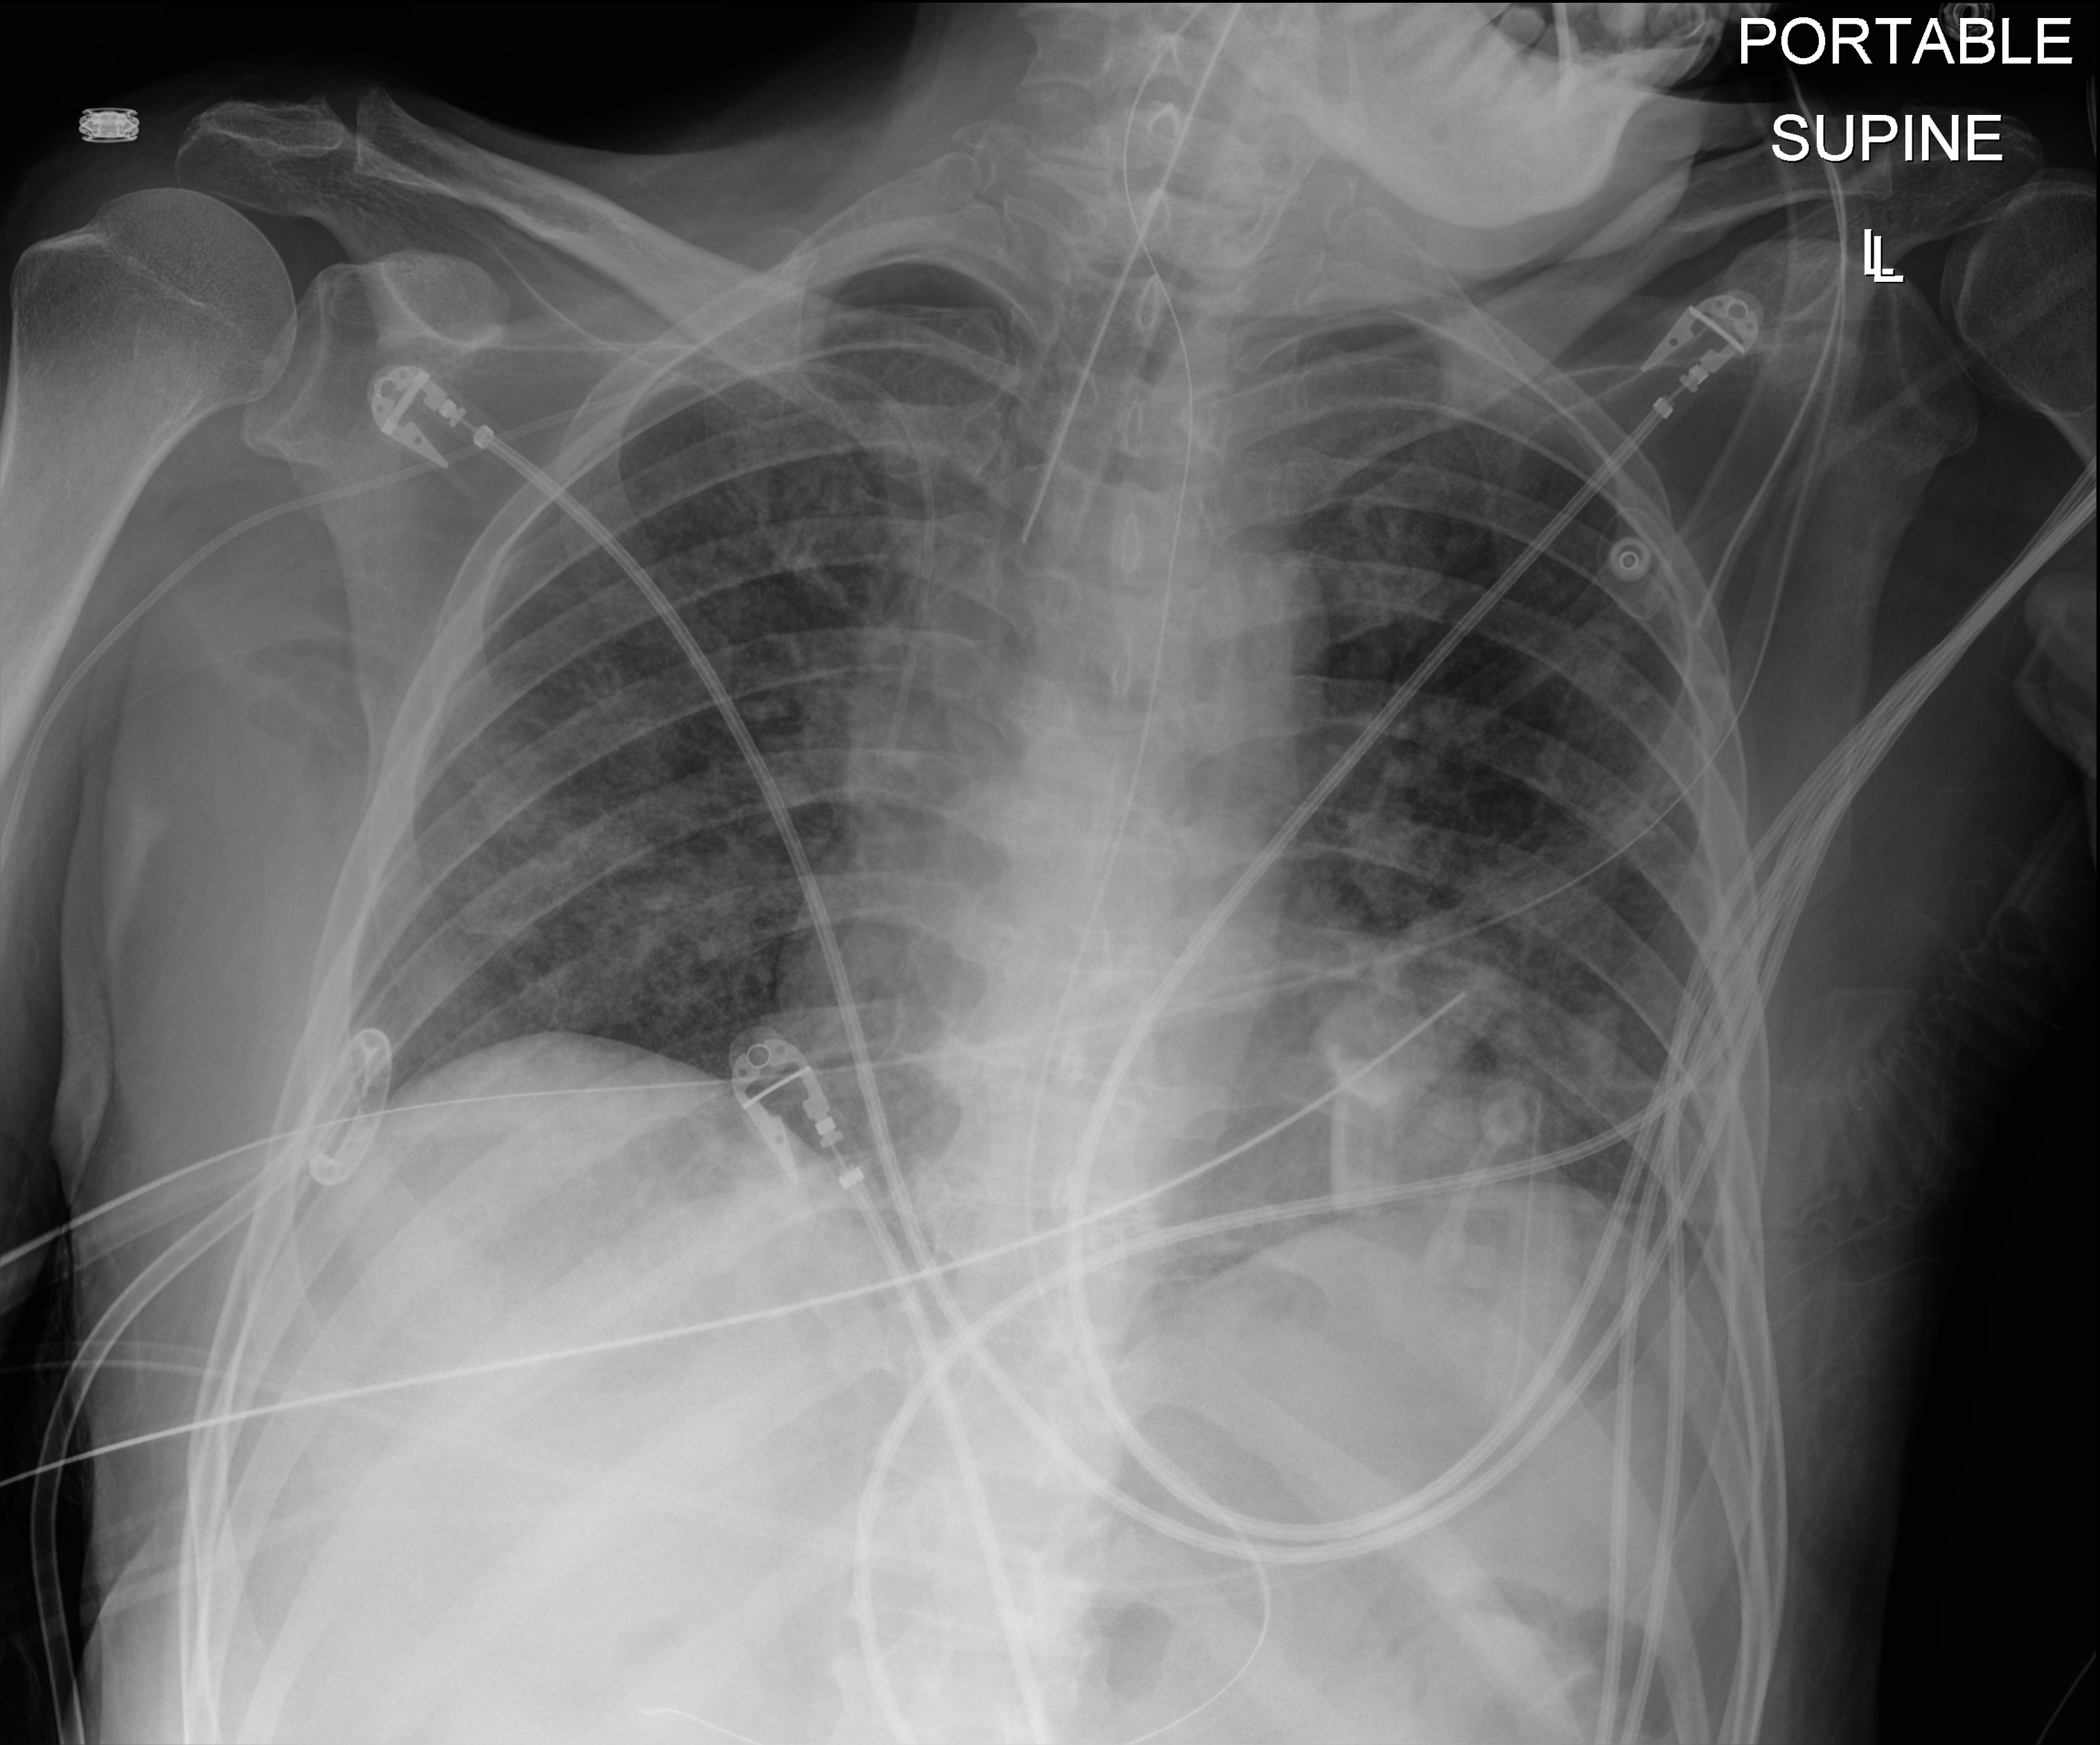
Chest X-ray (portable), anteroposterior (AP) projection. Patient hospitalised with COVID-19; male, aged 18–59 years.
Hospital-stay facts (about this admission, not read from this image; timing relative to this image not recorded): mechanically ventilated during this hospital stay: yes; COPD (admission record): no; admitted to intensive care during this hospital stay: yes.